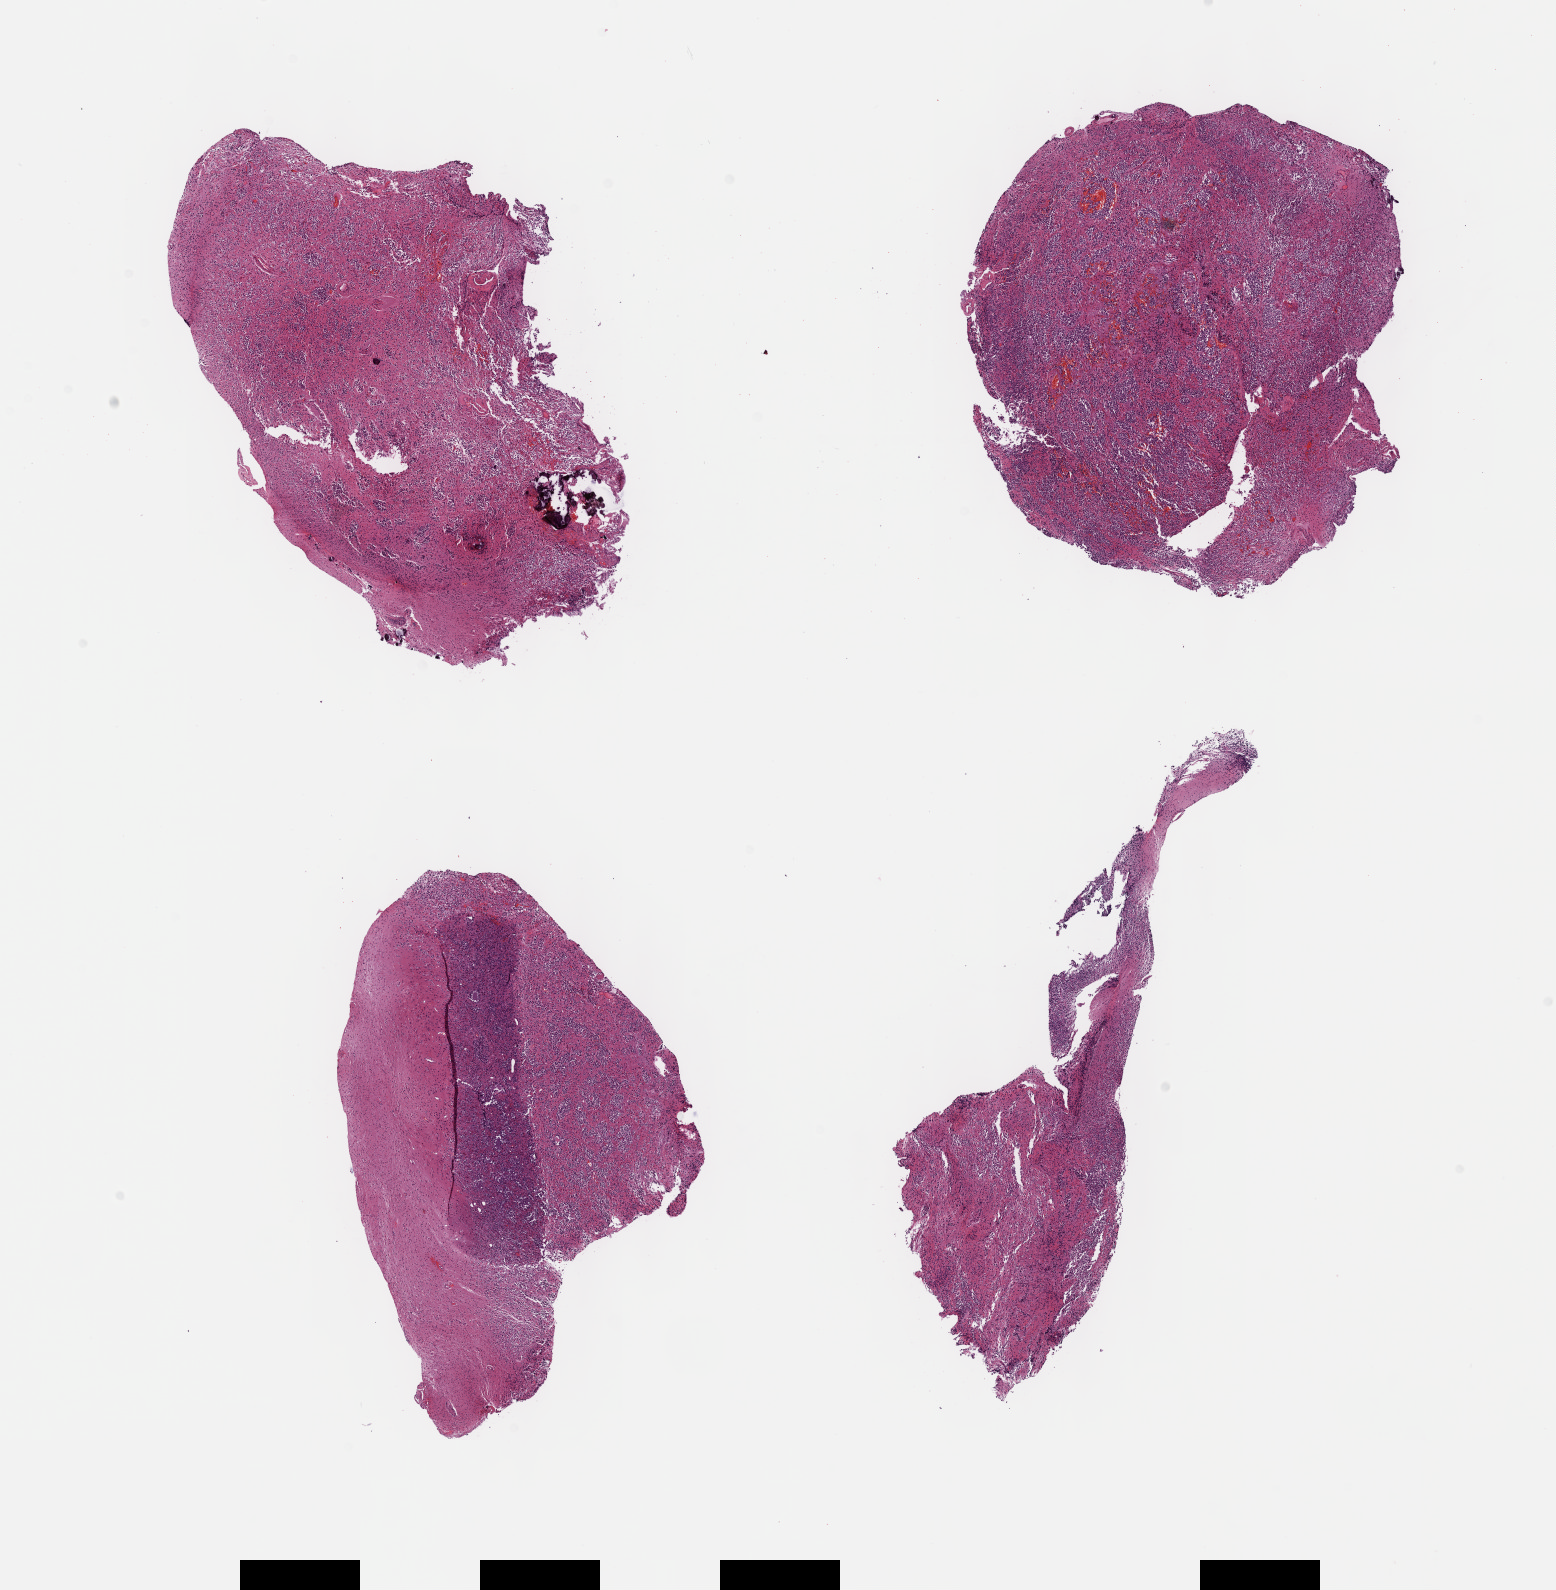
Whole-slide histology image, H&E, low-resolution overview of the scanned area, about 12.6 x 12.9 mm (acquisition: 40x scan), FFPE section, primary tumour sample from the brain. Male, age 53 years at initial diagnosis.
Pathologic diagnosis: Oligodendroglioma, anaplastic (cerebrum).